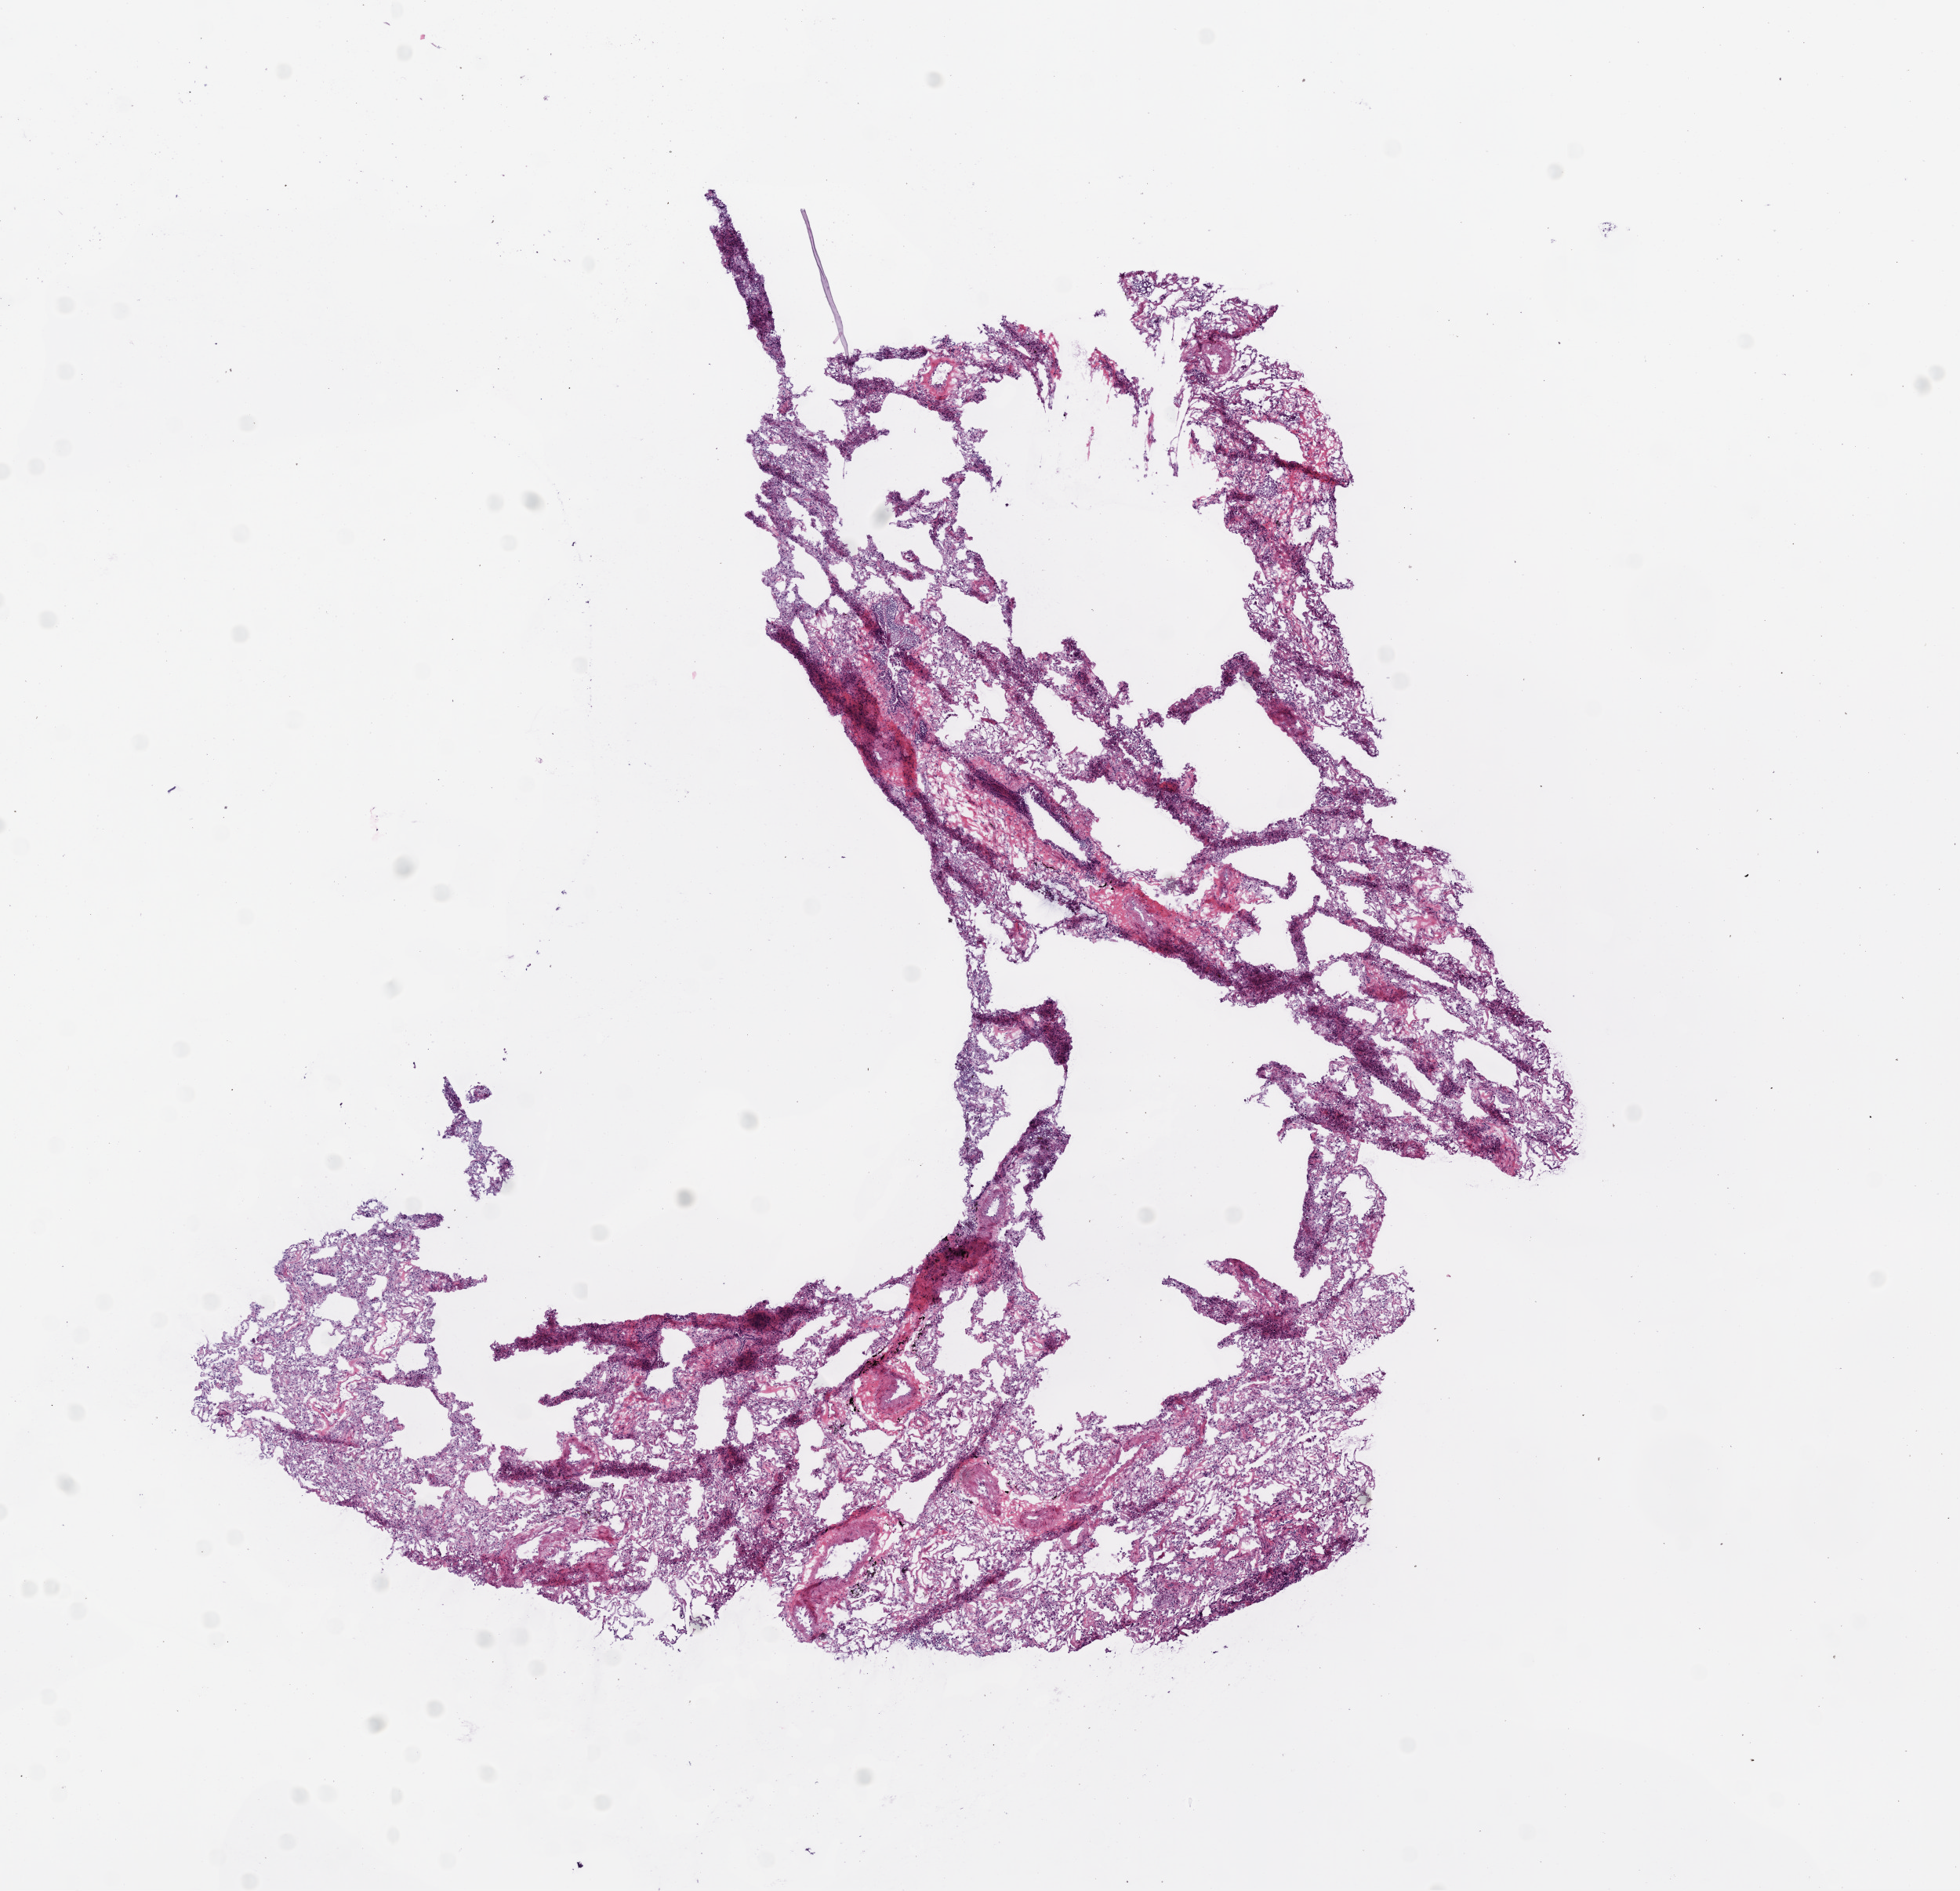
Whole-slide histology image, H&E-stained — whole scanned area (about 10.0 x 9.7 mm, acquisition: 20x scan) shown as a low-resolution overview. Frozen section. Lung, solid tissue normal (non-tumour tissue) sample. Male patient; age at initial diagnosis 83 years.
This section: solid tissue normal (non-tumour) sample from the same patient. Patient diagnosis: Squamous cell carcinoma, NOS.